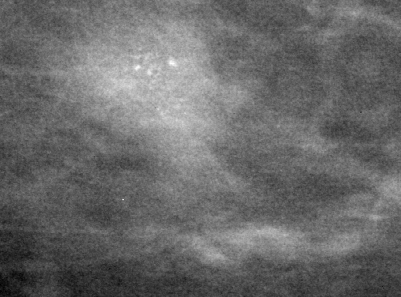
Region of interest cut from a scanned film mammogram (one marked finding), left breast, CC view, BI-RADS breast density category 2 (scale 1–4).
- Marked abnormality: calcifications, morphology pleomorphic, distribution clustered; BI-RADS assessment category 4; pathology (as recorded): benign.